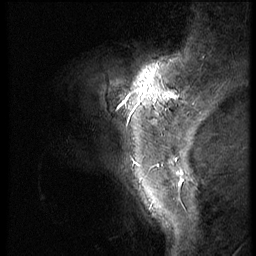
Breast MRI (dynamic contrast-enhanced), one sagittal slice. Slice 11 of 56 in the series (ordered by position). 3 images stored at this slice position (order not interpretable as contrast timing). 1.5 T. TE 4.2 ms, TR 9 ms. 2.5 mm slice thickness. 256 × 256 image matrix, field of view 180 × 180 mm. Patient: female, 46 years. Case-level facts recorded for this patient, not image findings: setting: breast cancer imaged before/during neoadjuvant chemotherapy; receptor status: HER2-positive.
Annotated regions visible in this slice (semi-automatic segmentation, software-assisted and operator-edited):
- analysis volume of interest (the breast-tissue region the enhancement analysis was run in; not a lesion): bounding box (x1, y1, x2, y2) in pixels: (79, 68, 190, 143)
- tumour enhancement mask (voxels above the 140 % enhancement threshold inside the analysis volume of interest): (123, 90, 178, 104)